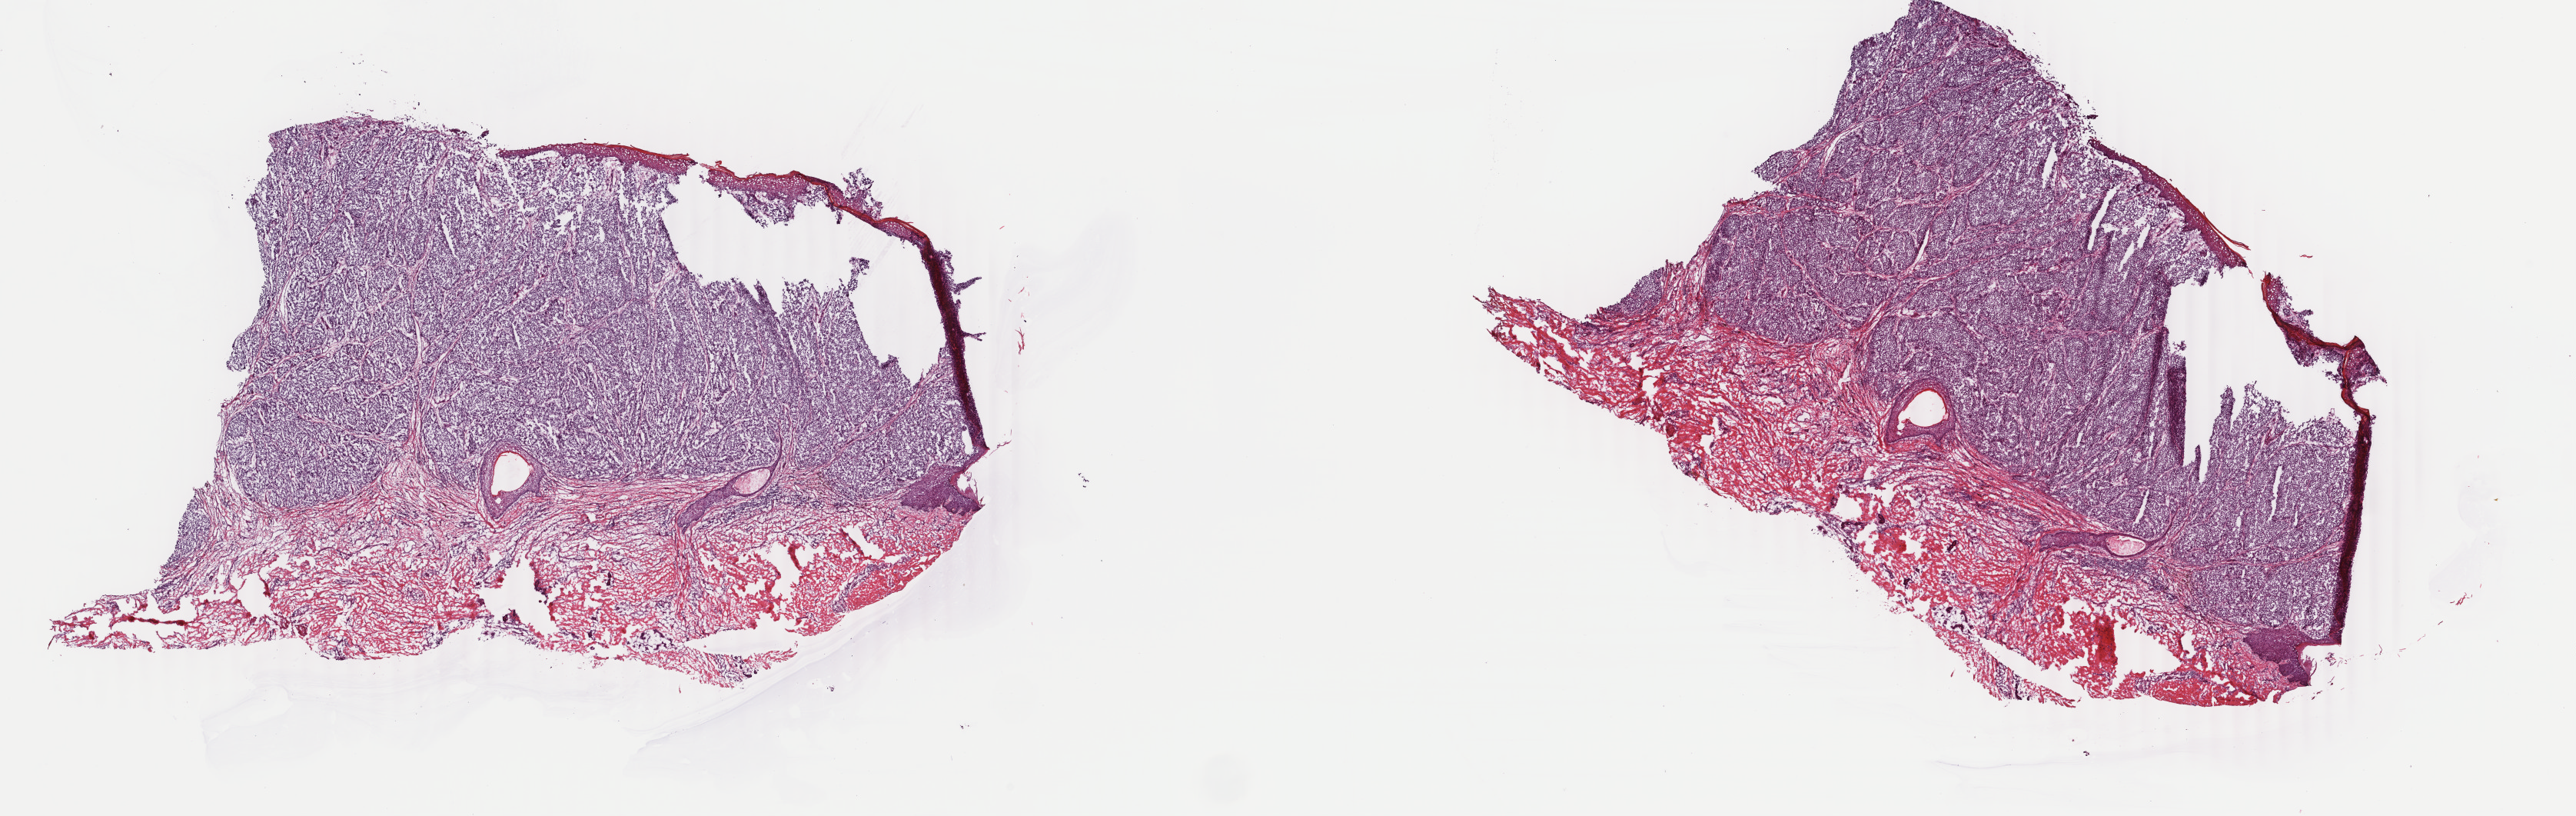
Whole-slide histology image, Hematoxylin and eosin (H&E) stained — whole scanned area (about 26.7 x 8.4 mm) shown as a low-resolution overview; frozen section from the top of the tissue portion; skin, primary tumour sample. Male, age 73 years at initial diagnosis. Slide review estimates, as recorded: tumour cells 80%, tumour nuclei 90%, normal cells 20%, stromal cells 0%, necrosis 0%. Inflammatory infiltration, as recorded: lymphocyte infiltration 0%, monocyte infiltration 0%, neutrophil infiltration 0%.
TNM: T3b NX M0. Diagnosis: Nodular melanoma. AJCC pathologic stage: IIB (7th edition).